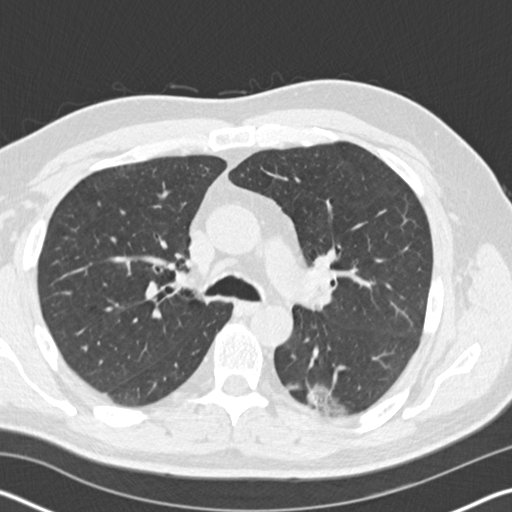
Axial slice from a low-dose chest CT screening exam; first (baseline) screen; lung window (W 1500 / L -600 HU); 2 mm slice thickness; standard (soft-tissue) reconstruction kernel (B30f). Male participant, aged 60 years at enrolment. Current smoker at enrolment.
- Expert reader's lesion annotation, bounding box (x1, y1, x2, y2) in pixels: (277, 363, 358, 425).
- The screening reader recorded 3 non-calcified nodules or masses ≥4 mm on this exam (left lower lobe, right lower lobe, right lower lobe); which of them this box marks is not recorded.
- Official screen result: positive, change unspecified: nodule(s) >= 4 mm or enlarging nodule(s), mass(es), or other non-specific abnormalities suspicious for lung cancer.
- Lung cancer was diagnosed 171 days after this screen: papillary adenocarcinoma, NOS, left lower lobe, moderately differentiated (G2), stage IB (AJCC 6th edition), 35 mm at pathology.